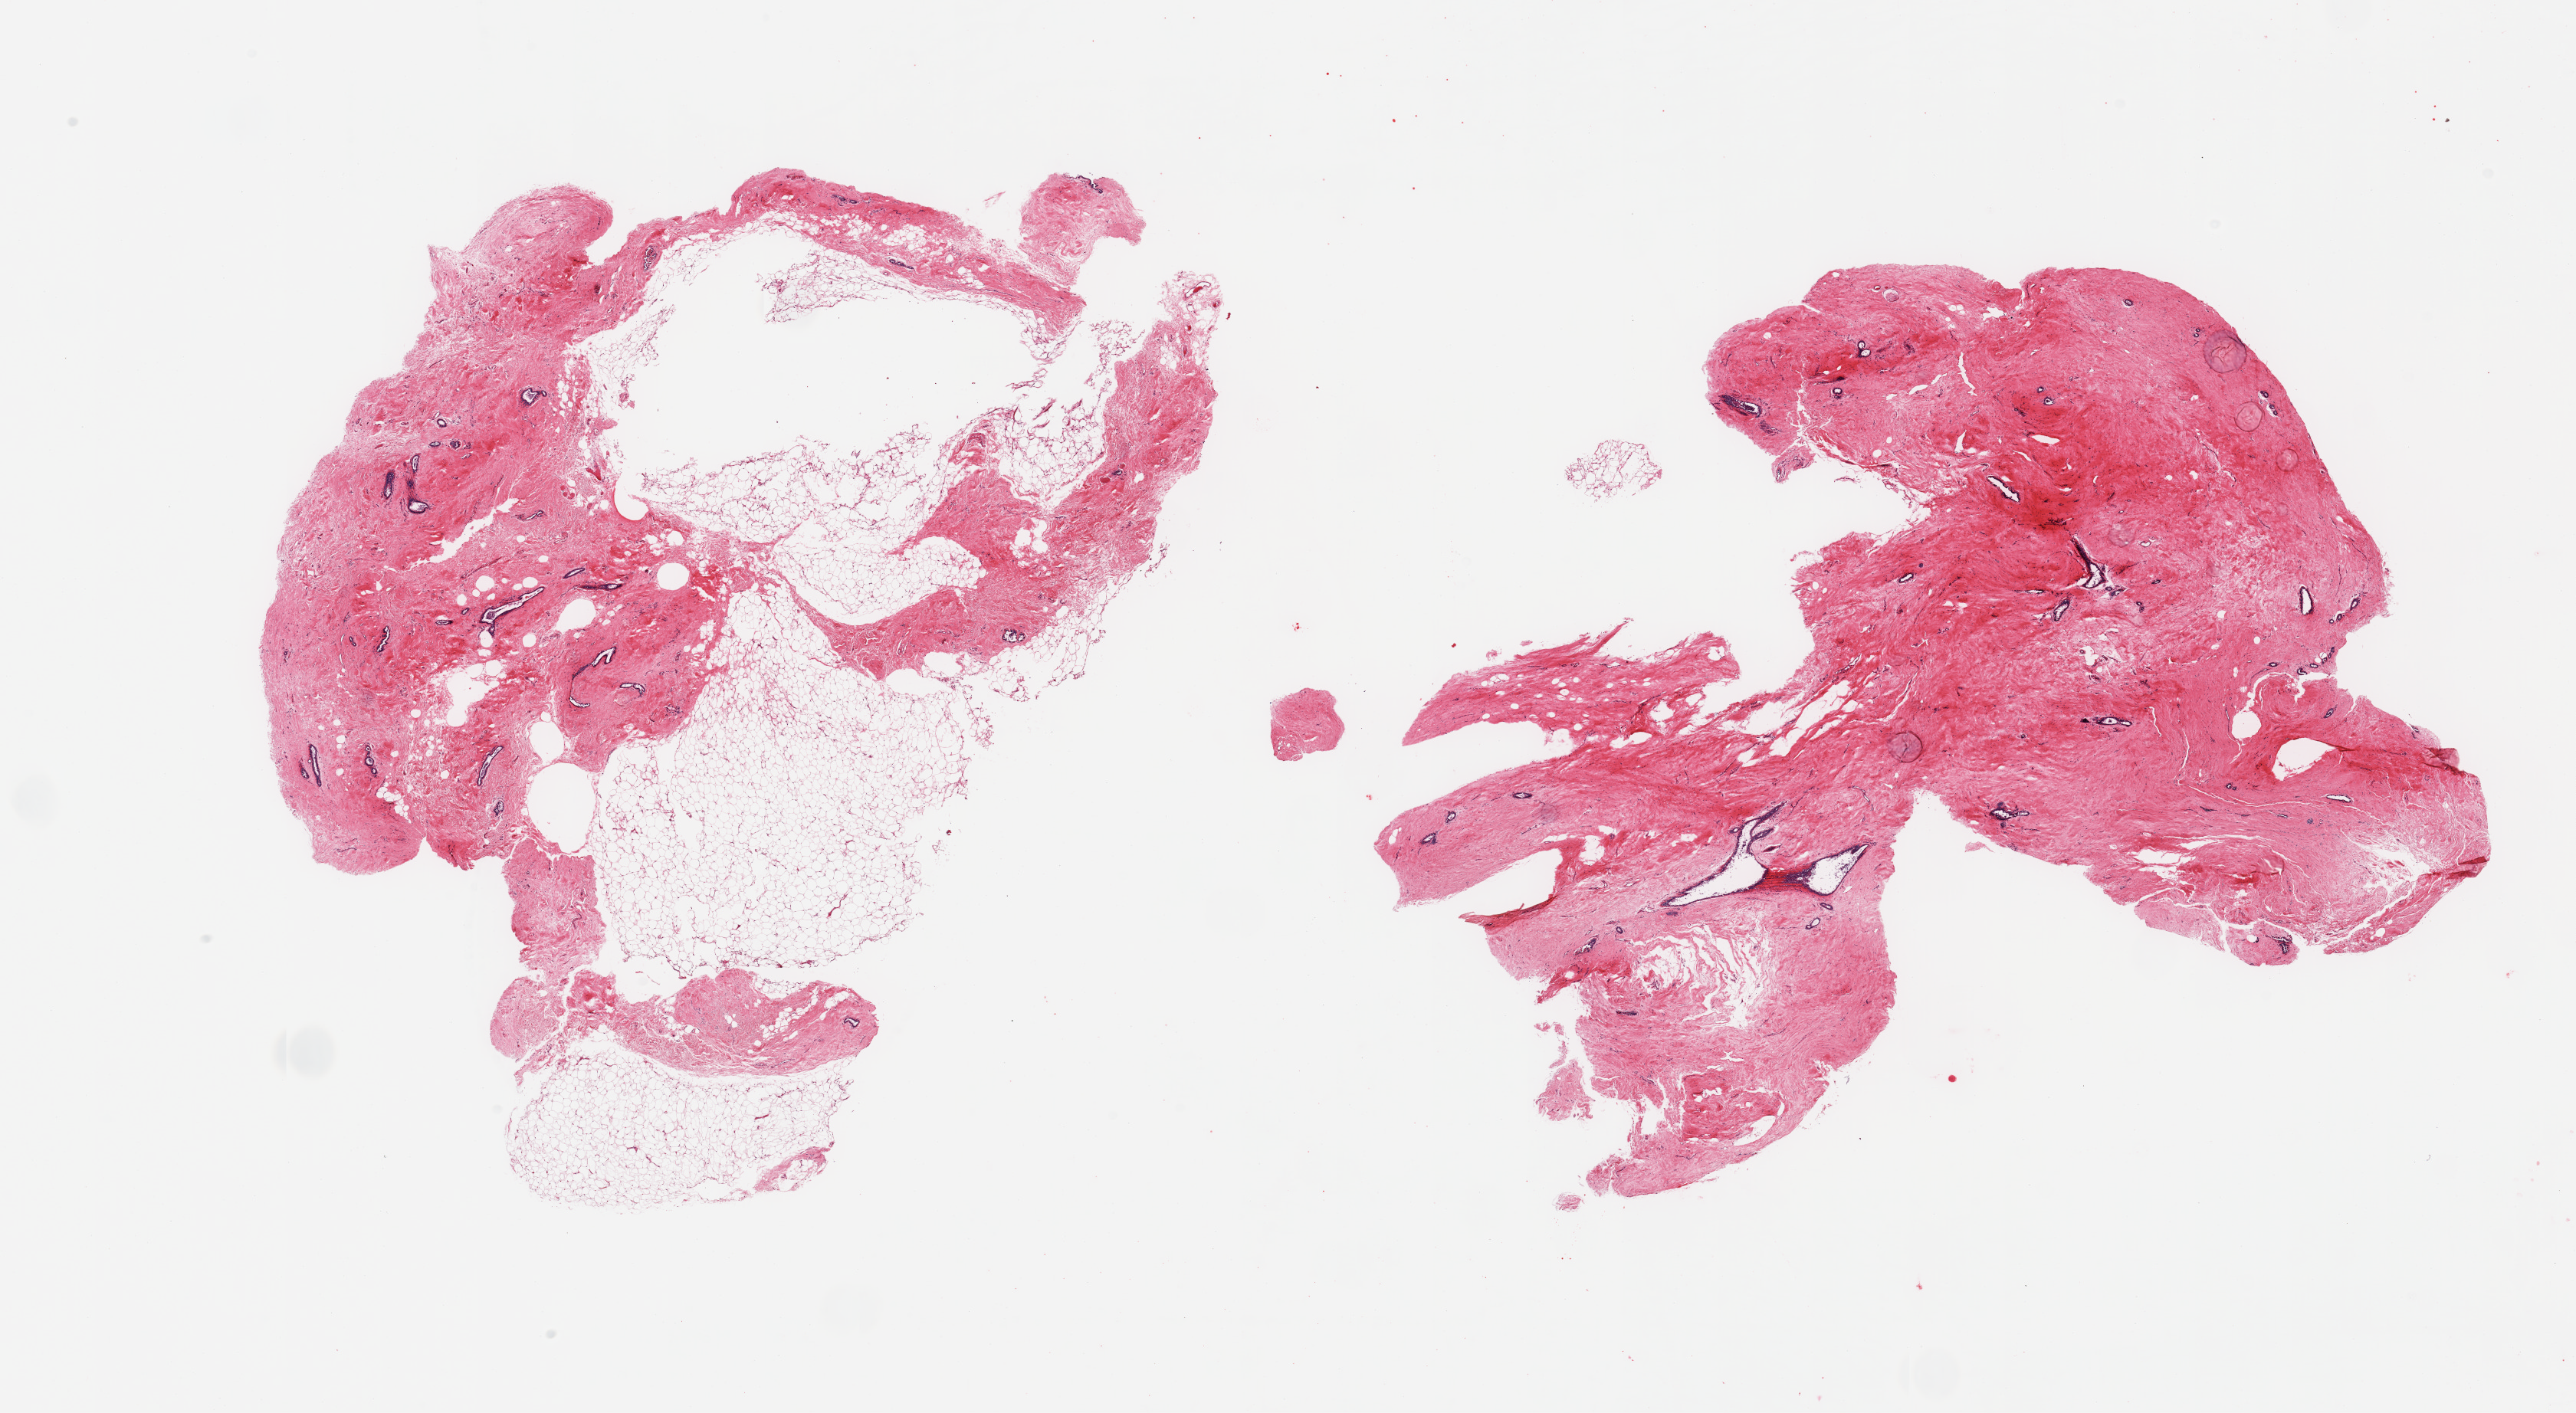
Digitized hematoxylin and eosin (H&E)-stained section, low-resolution overview of the scanned area, about 26.6 x 14.6 mm; PAXgene-fixed, paraffin-embedded tissue; target tissue: breast; tissue donor sample. Donor: male.
Reviewer comment on this tissue sample: 2 pieces, prominent stromal and ductal gynecomastoid hyperplasia.